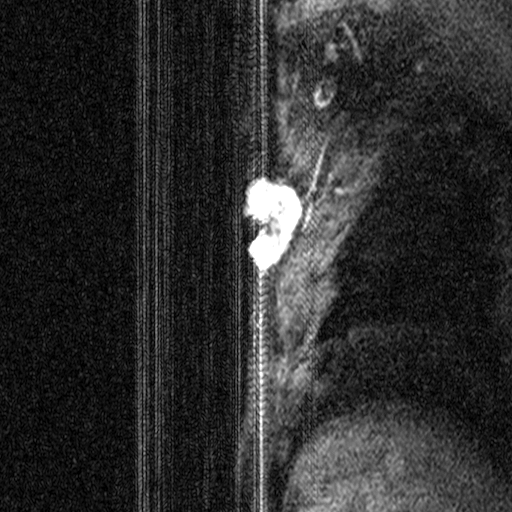
Breast MRI (dynamic contrast-enhanced), one sagittal slice. Dynamic contrast-enhanced study with each time point stored as its own series, time point 2 of 3 at this slice position (early post-contrast, ordered by acquisition time). 1.5 T. TE 4.5 ms, TR 11 ms. 3 mm slice thickness. 512 × 512 image matrix, field of view 200 × 200 mm. Female patient, age 44 years. From the clinical record (not read from this slice): setting: breast cancer imaged before/during neoadjuvant chemotherapy; receptor status: HR-positive, HER2-negative.
Structures marked on this image (semi-automatically segmented with operator editing):
- analysis volume of interest (the breast-tissue region the enhancement analysis was run in; not a lesion): box from (x=206, y=164) to (x=312, y=299) px
- tumour enhancement mask (voxels above the 90 % enhancement threshold inside the analysis volume of interest): (x=245, y=164)–(x=305, y=268)